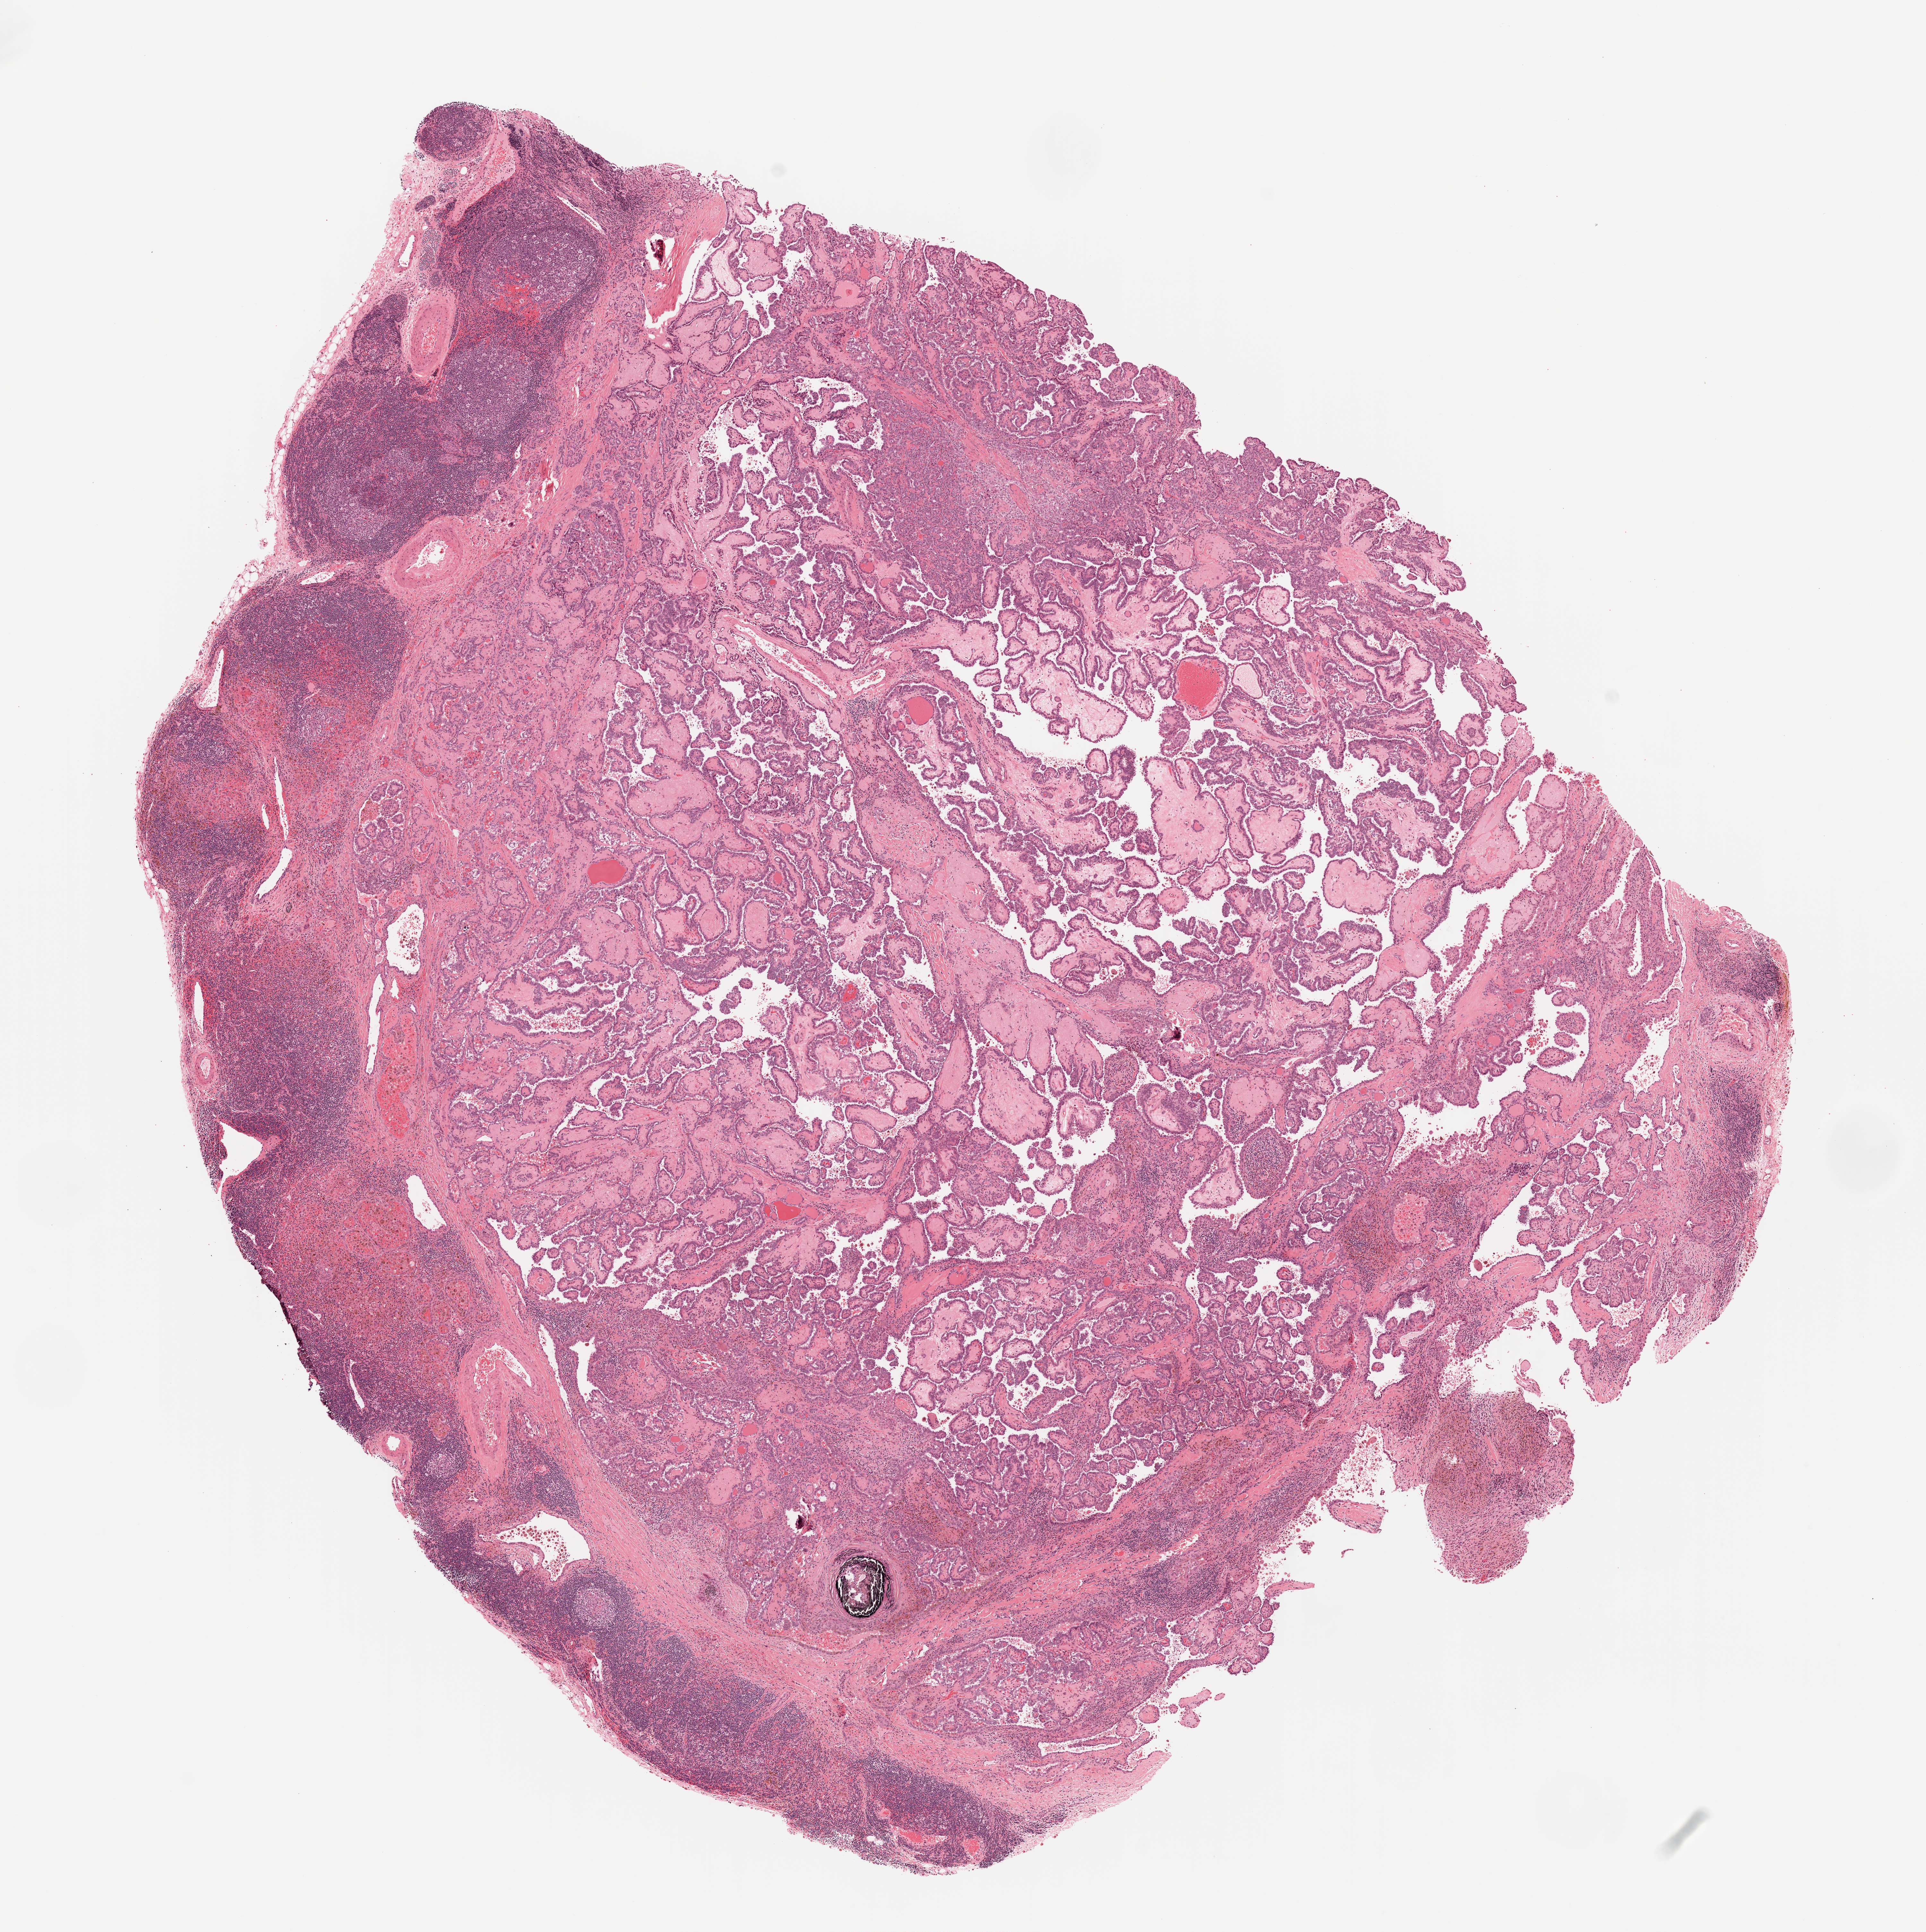
Digitized H&E tissue section (whole slide), whole scanned area (about 12.0 x 12.1 mm) shown as a low-resolution overview; formalin-fixed paraffin-embedded (FFPE) diagnostic section; primary tumour sample from the thyroid. Female, age 43 years at initial diagnosis.
AJCC pathologic stage: I (7th edition). Laterality: right. Diagnosis: Papillary adenocarcinoma, NOS.